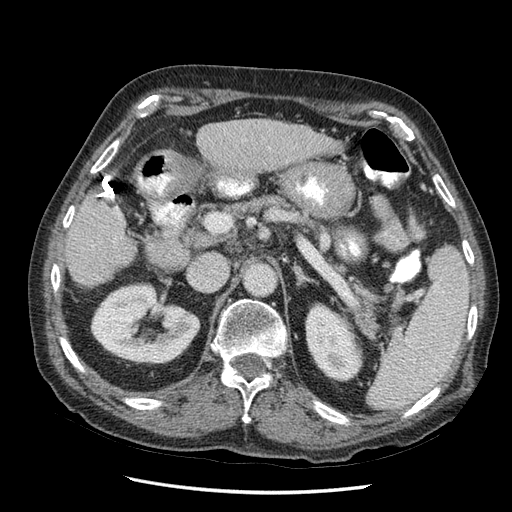
Contrast-enhanced abdominal CT (liver protocol), one axial slice; slice 20 of 67 in the series (ordered by position); reconstruction kernel STANDARD; 120 kVp; soft-tissue window (W 400 / L 40 HU); 2.5 mm slice thickness; 512 × 512 image matrix, field of view 360 × 360 mm. Case-level facts recorded for this patient, not image findings: diagnosis: hepatocellular carcinoma (patient treated with transarterial chemoembolisation; whether this scan precedes or follows treatment is not stated here); TNM stage (as recorded): Stage-I; Child-Pugh class: A; tumour differentiation: moderately differentiated.
Outlined on this slice (semi-automatic segmentation, software-assisted and operator-edited):
- liver parenchyma outside the tumour (the mass and vessels are separate outlines, so this box may not span the whole liver): bounding box <66,120,337,290> (left, top, right, bottom; pixels)
- liver vessels: <99,199,118,246>